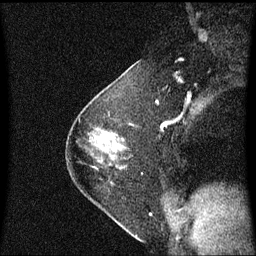
Breast MRI (dynamic contrast-enhanced), one sagittal slice; dynamic contrast-enhanced series, image 2 of 3 at this slice position (ordered by acquisition); 1.5 T; TE 4.2 ms, TR 8.4 ms; 256 × 256 image matrix. Female patient, age 54 years. Case-level facts recorded for this patient, not image findings: setting: breast cancer imaged before/during neoadjuvant chemotherapy; receptor status: HER2-positive.
Structures marked on this image (semi-automatically segmented with operator editing):
- analysis volume of interest (the breast-tissue region the enhancement analysis was run in; not a lesion): bounding box [x1, y1, x2, y2] px = [92, 132, 126, 170]
- tumour enhancement mask (voxels above the 70 % enhancement threshold inside the analysis volume of interest): [103, 133, 111, 142]